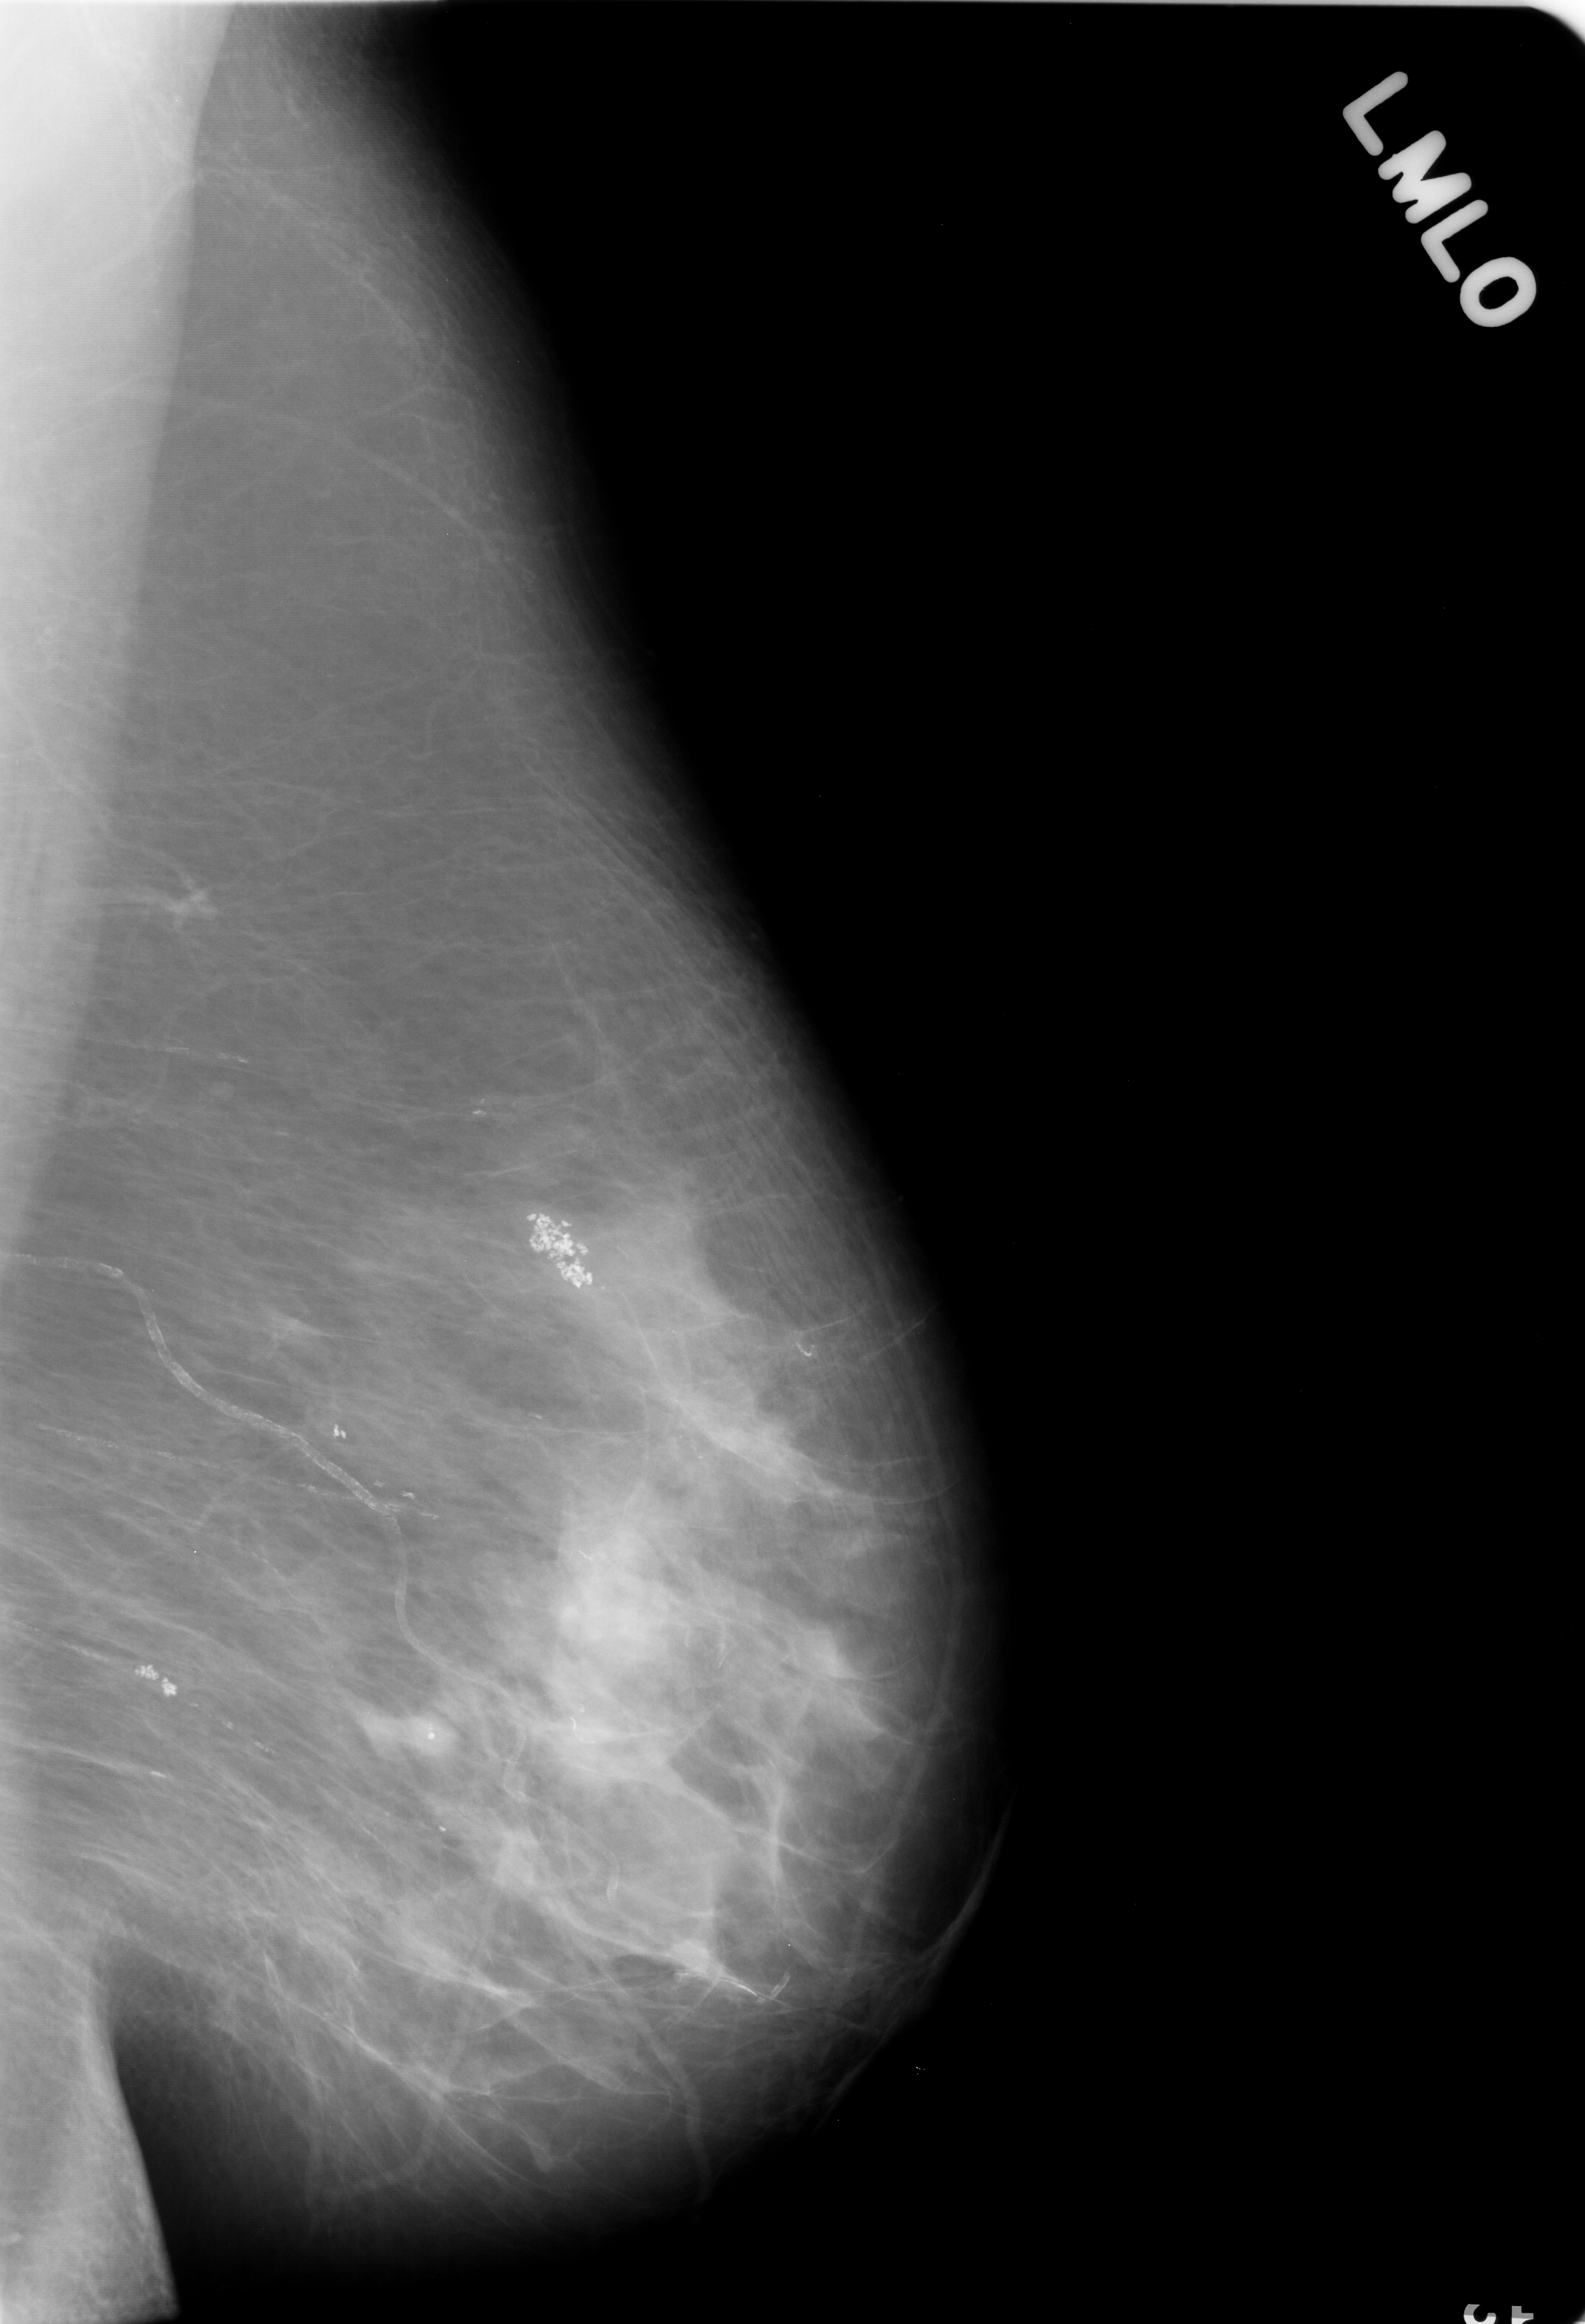
Digitized screen-film mammogram; left breast; mediolateral oblique (MLO) view.
- Abnormality record for this image: Finding 1 of 2: calcifications, morphology pleomorphic, distribution clustered; BI-RADS assessment category 4; pathology (as recorded): benign.
- Finding 2 of 2: calcifications, morphology pleomorphic, distribution clustered; BI-RADS assessment category 4; subtlety rating 5 on a 1 (subtle) to 5 (obvious) scale; pathology result (as recorded, not read from the image): benign.